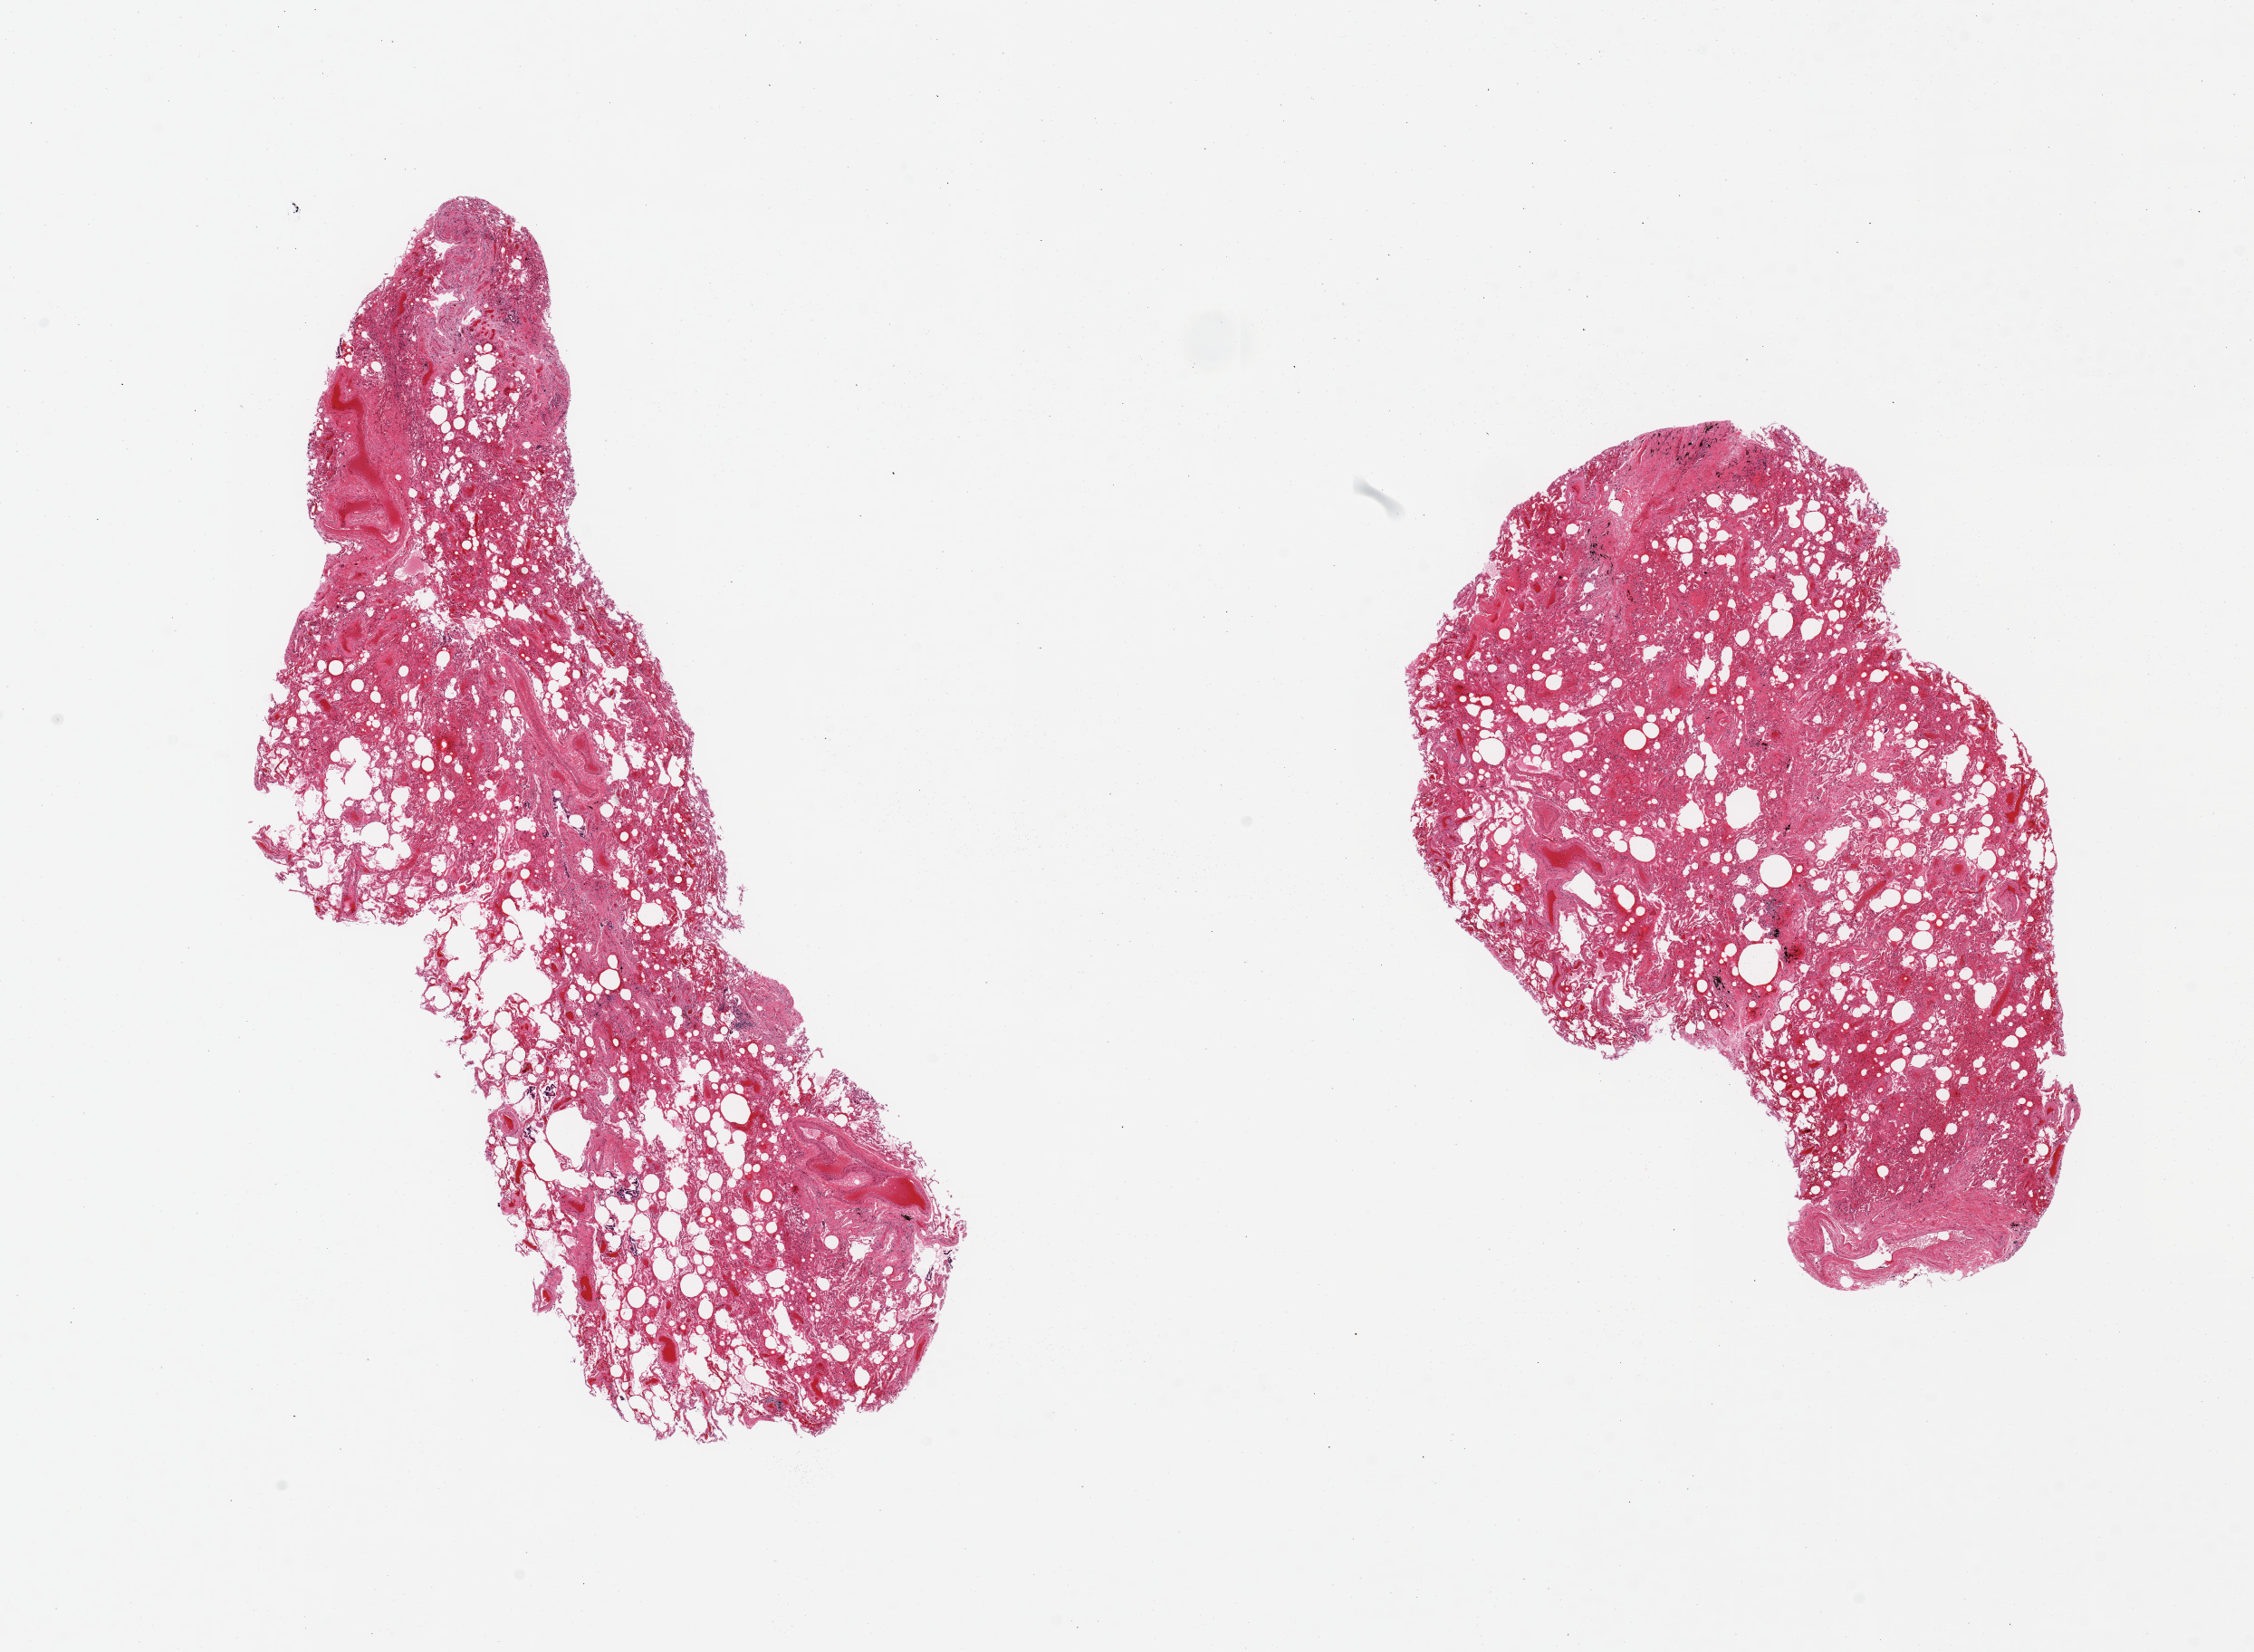
Digitized hematoxylin and eosin (H&E)-stained section, brightfield — shown as a low-resolution overview of the whole scanned area (about 19.7 x 14.4 mm). PAXgene-fixed, paraffin-embedded tissue. Sampled site (target tissue): lung. Donor tissue sample. Donor: male.
Pathologist's review note for this sample: 2 pieces, moderate congestion.